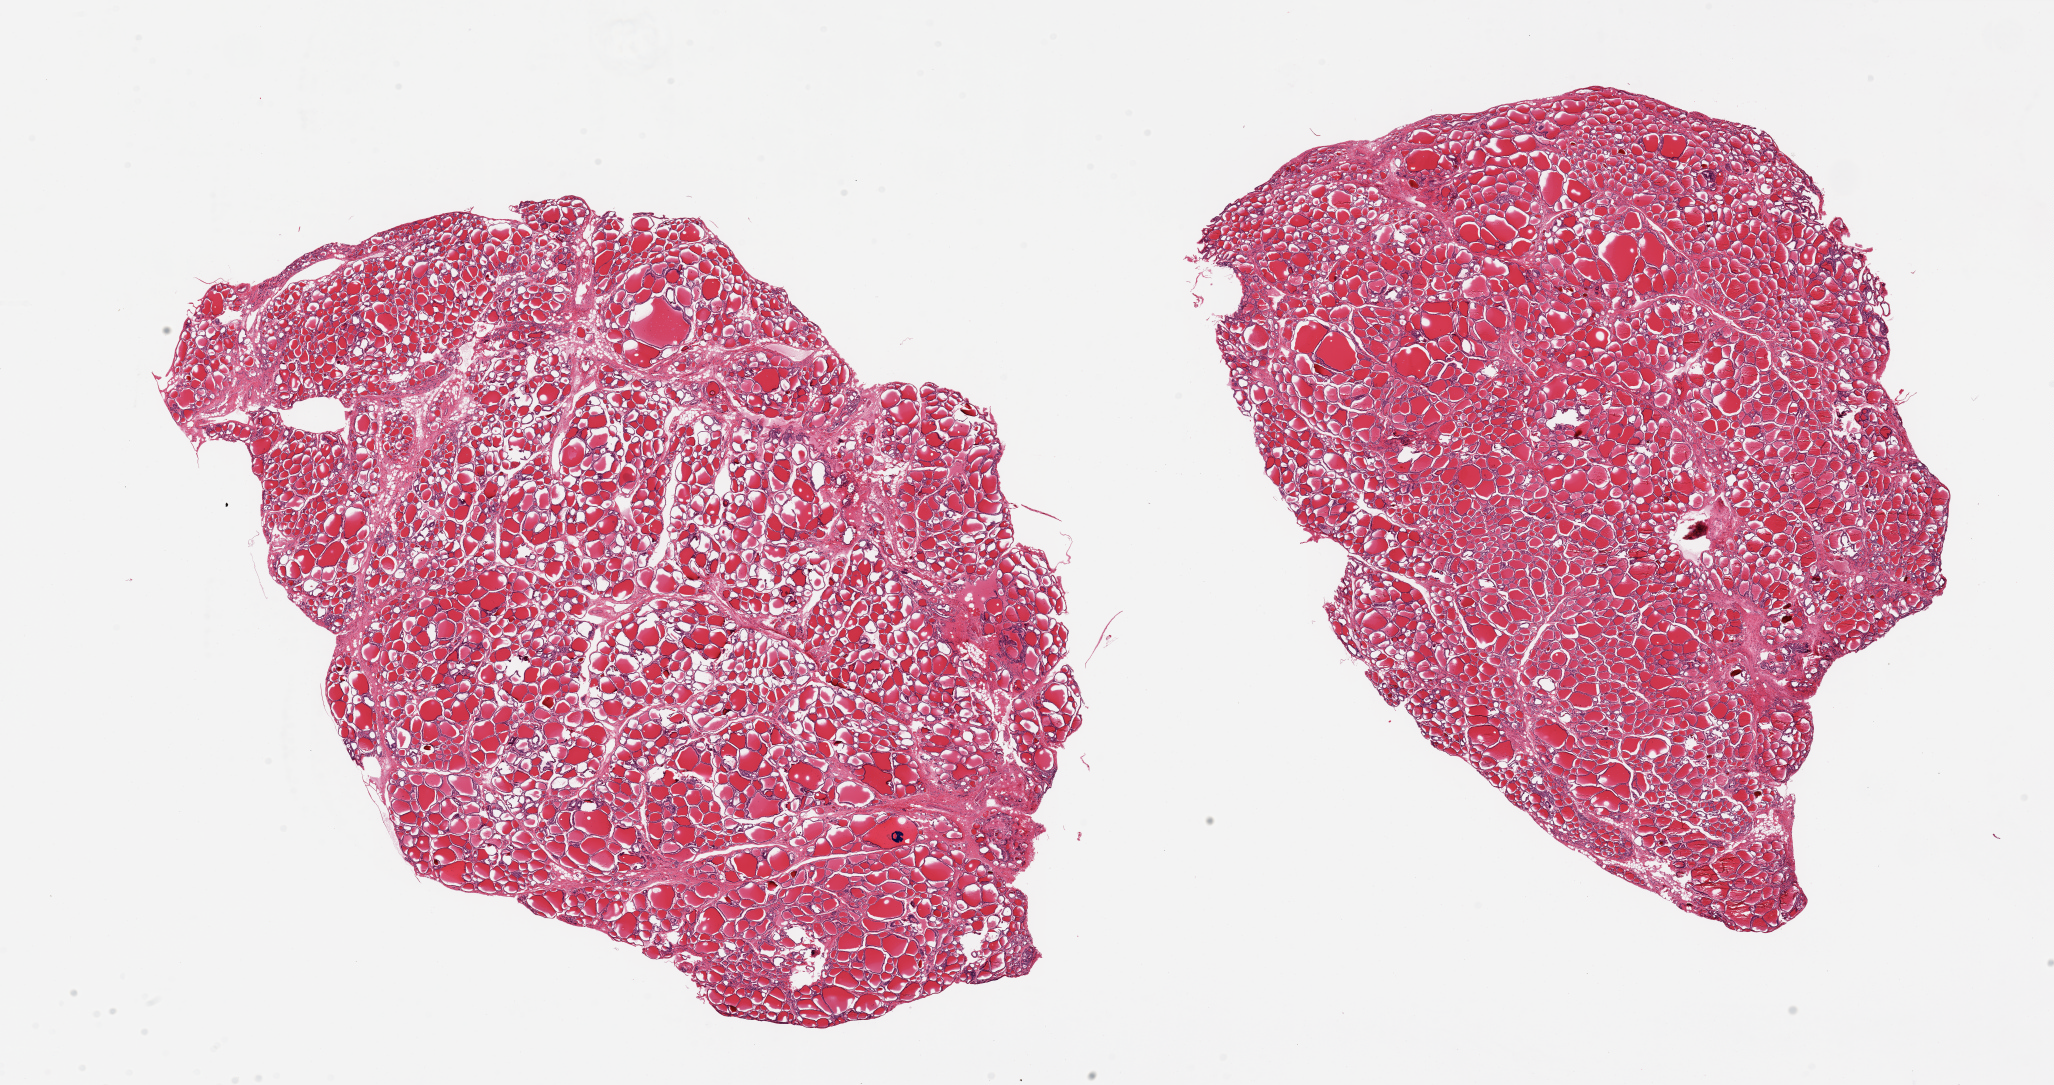
Hematoxylin and eosin (H&E) whole-slide image, brightfield — low-resolution overview of the scanned area, about 32.5 x 17.2 mm (acquisition: 20x scan); PAXgene-fixed, paraffin-embedded tissue; section of thyroid (target tissue); donor tissue sample. Female donor.
Reviewer comment on this tissue sample: 2 pieces, 17x11.5 & 14.5x10mm; no significant inflammation noted.